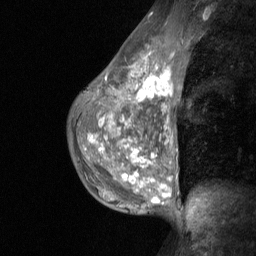
Breast MRI (dynamic contrast-enhanced), one sagittal slice. Slice 39 of 64 in the series (ordered by position). Dynamic contrast-enhanced study with each time point stored as its own series, time point 2 of 3 at this slice position (early post-contrast, ordered by acquisition time). 1.5 T. TE 4.8 ms, TR 27 ms. 2 mm slice thickness. 256 × 256 image matrix, field of view 200 × 200 mm. Patient: female, 36 years. Case-level facts recorded for this patient, not image findings: setting: breast cancer imaged before/during neoadjuvant chemotherapy; receptor status: HR-positive, HER2-negative.
Annotated regions visible in this slice (semi-automatically segmented with operator editing):
- analysis volume of interest (the breast-tissue region the enhancement analysis was run in; not a lesion): bounding box [x1, y1, x2, y2] px = [73, 45, 182, 210]
- tumour enhancement mask (voxels above the 90 % enhancement threshold inside the analysis volume of interest): [90, 67, 172, 203]